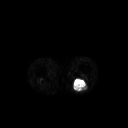
FDG PET of an extremity soft-tissue mass (from a PET/CT study), one axial slice; slice 193 of 267 in the series (ordered by position); 3.27 mm slice thickness; 128 × 128 image matrix, field of view 500 × 500 mm. Patient: male, 54 years. From the clinical record (not read from this slice): histological type: synovial sarcoma; site of the primary tumour: left poplietal fossa.
Outlined on this slice (expert contour drawn on MRI and transferred to this co-registered scan by the dataset authors):
- gross tumour volume (mass): box from (x=72, y=79) to (x=89, y=93) px